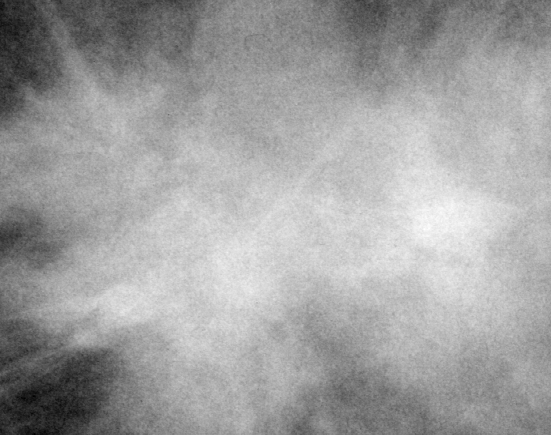
Cropped region of a digitized screen-film mammogram centred on a radiologist-marked abnormality, left breast, CC view, BI-RADS breast density category 2 (scale 1–4).
Marked abnormality: mass, shape irregular / architectural distortion, margins spiculated; BI-RADS assessment category 5; subtlety rating 5 on a 1 (subtle) to 5 (obvious) scale; pathology result (as recorded, not read from the image): malignant.